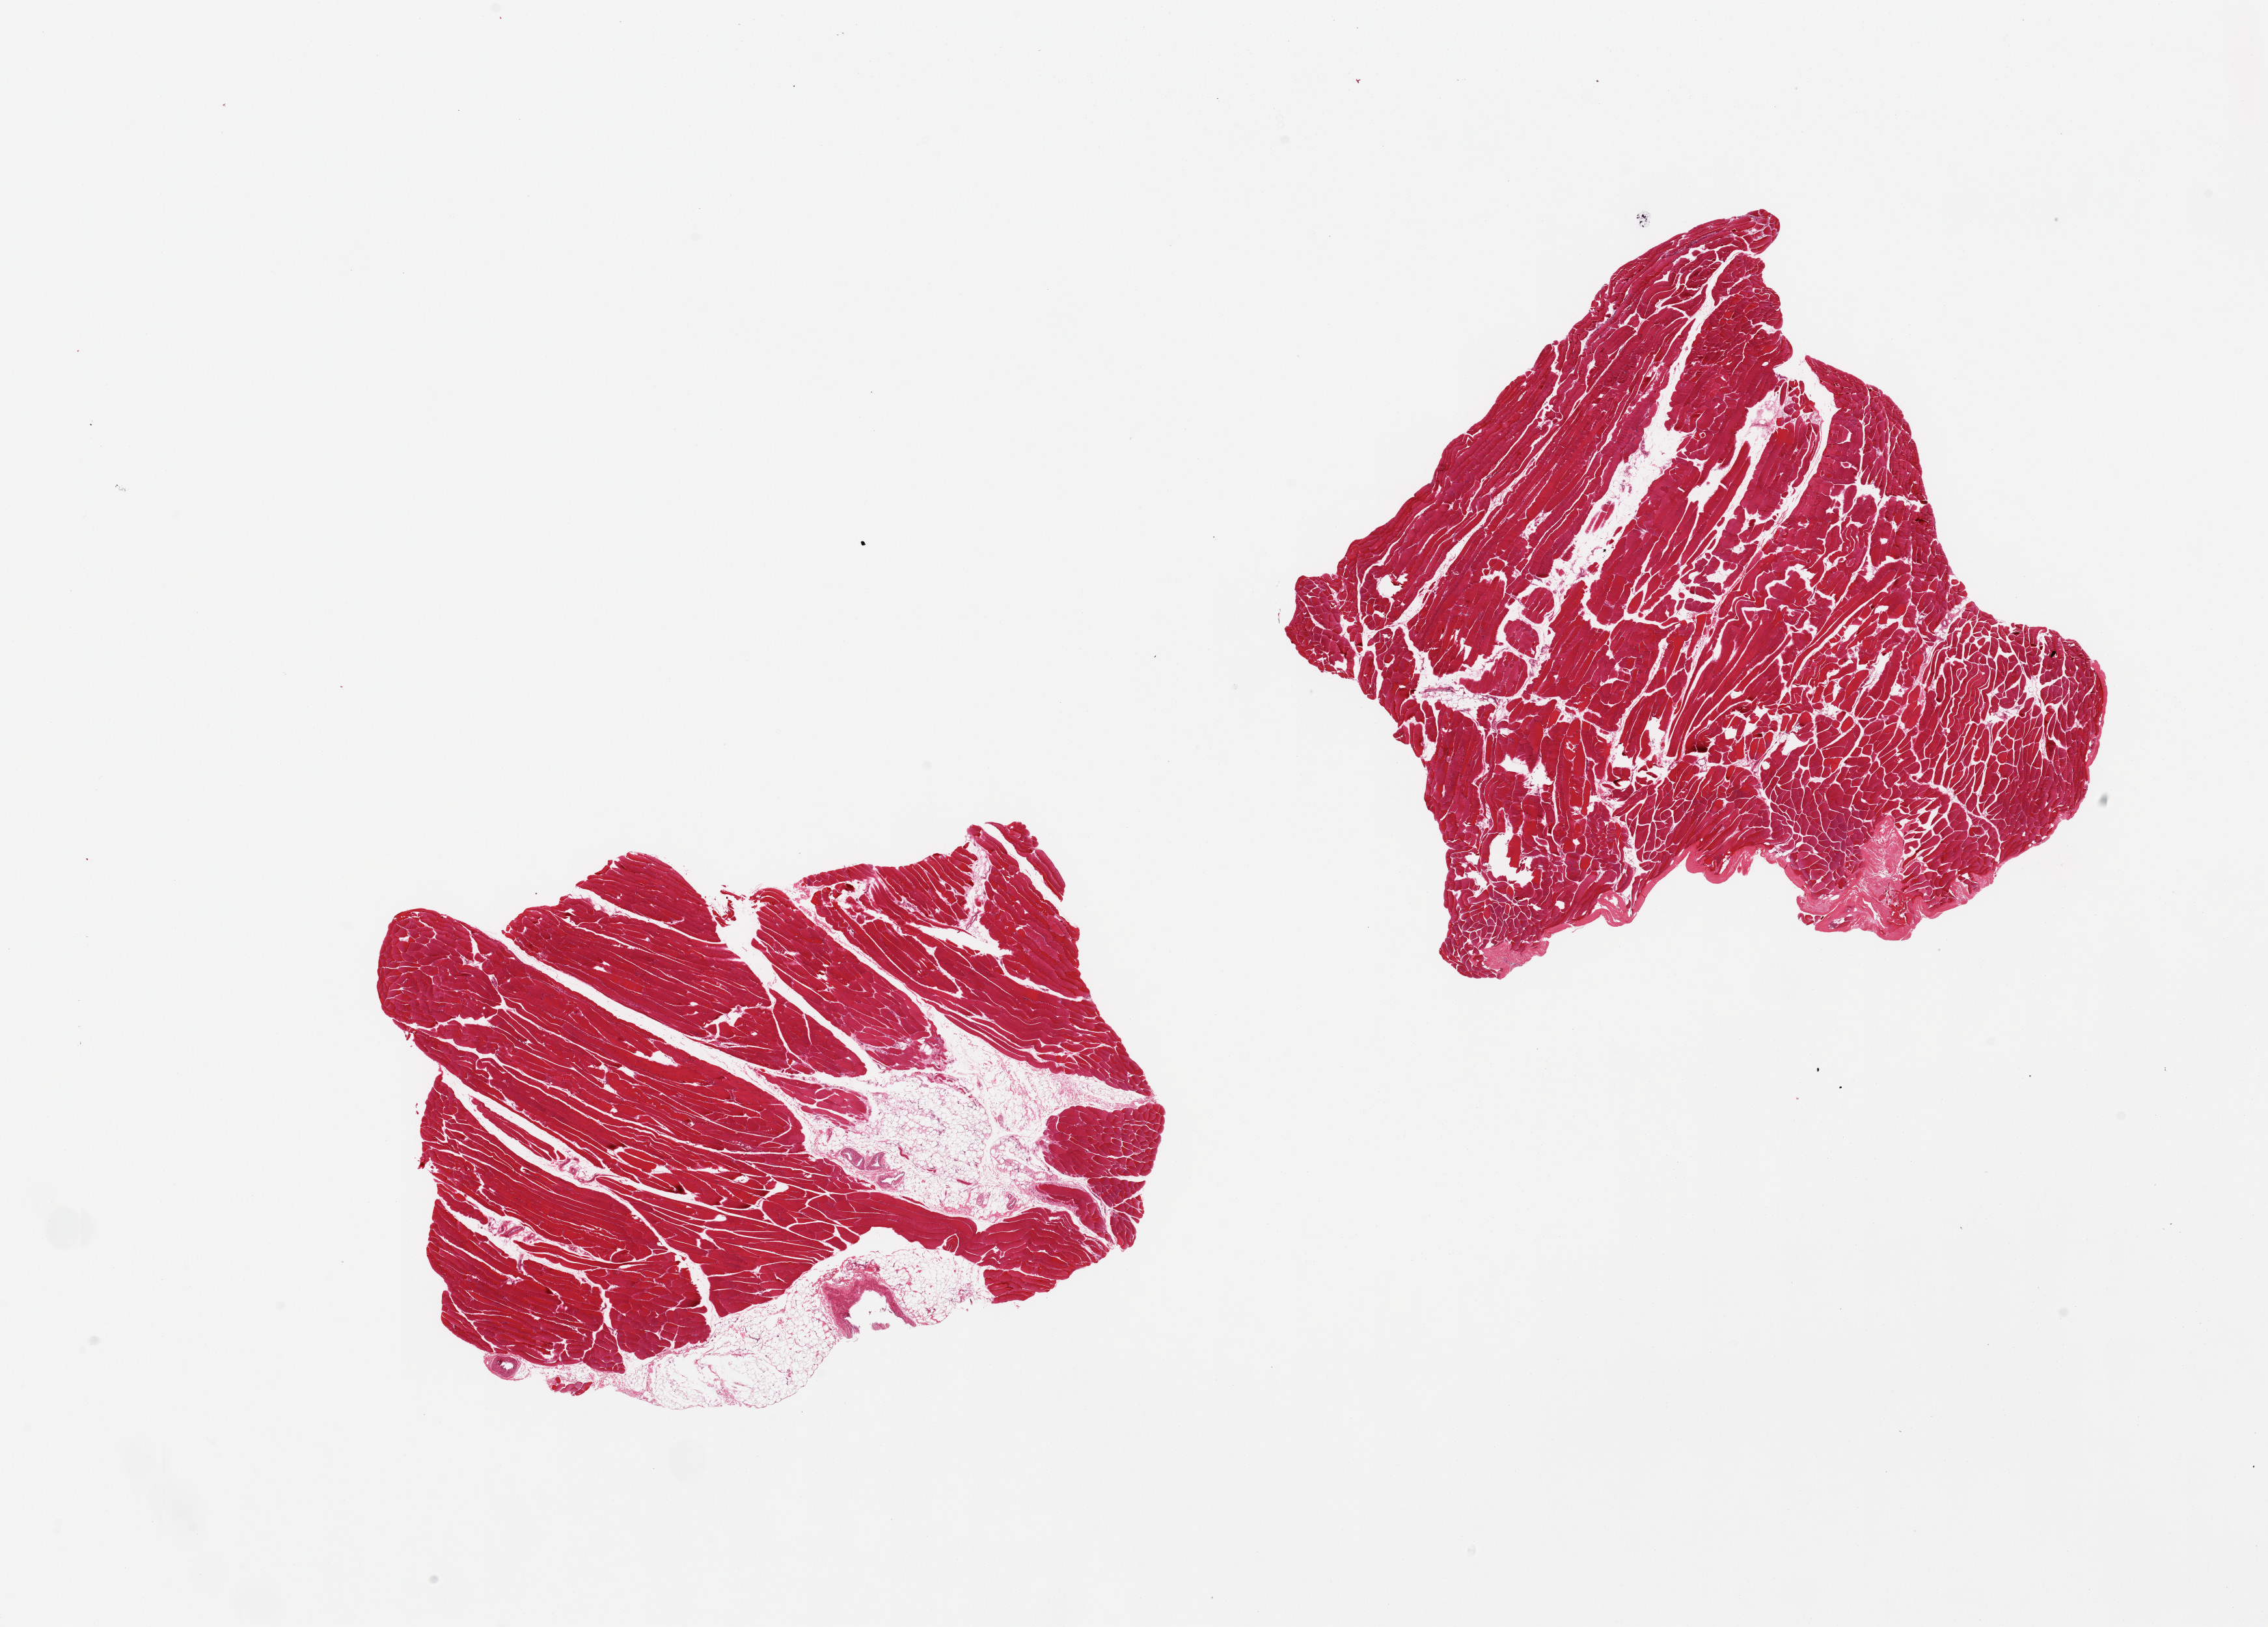
Whole-slide image, hematoxylin and eosin (H&E) stain — whole scanned area (about 27.6 x 19.8 mm, slide scanned at 20x) shown as a low-resolution overview. PAXgene-fixed, paraffin-embedded tissue. Section of skeletal muscle (target tissue). Tissue donor sample. Donor sex: male.
• reviewer comment on this tissue sample: 2 pieces, 9x7 & 9x9mm; focal atrophy; 1 has 20% internal and external adipose